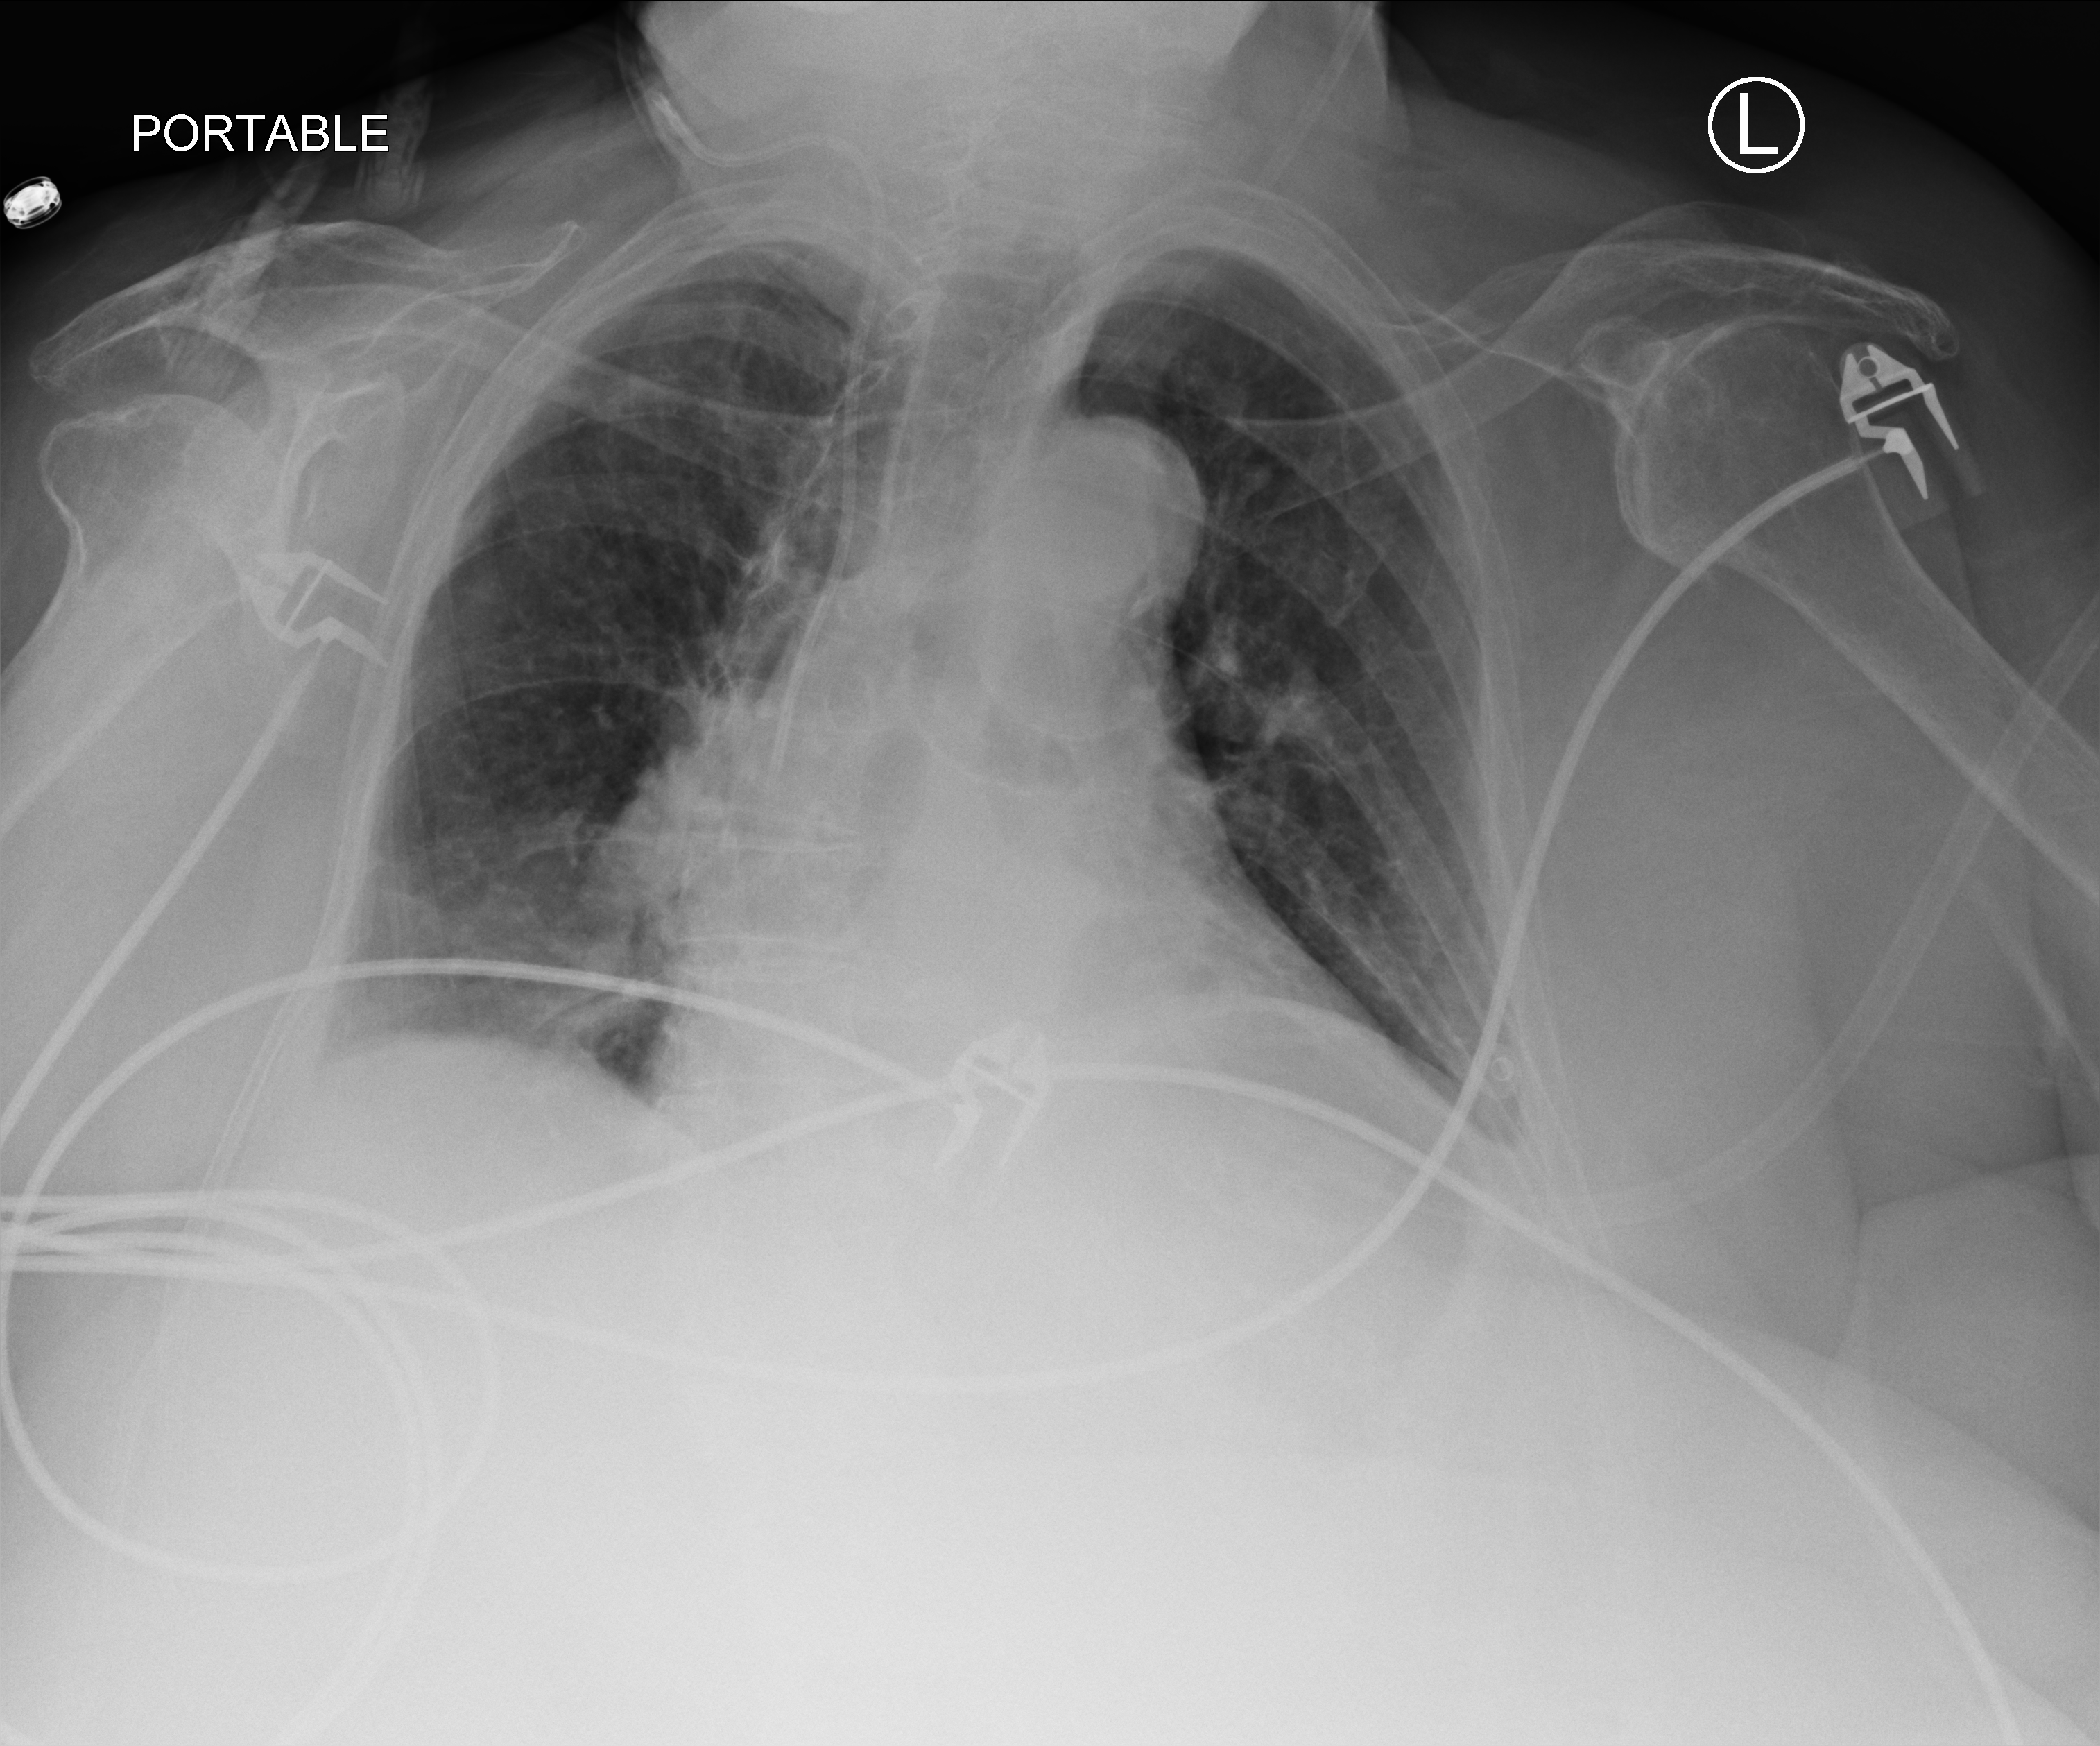
Chest X-ray (portable), anteroposterior (AP) projection. Patient hospitalised with COVID-19; female, aged 75–90 years.
Hospital-stay facts (about this admission, not read from this image; timing relative to this image not recorded):
- admitted to intensive care during this hospital stay: yes
- mechanically ventilated during this hospital stay: no